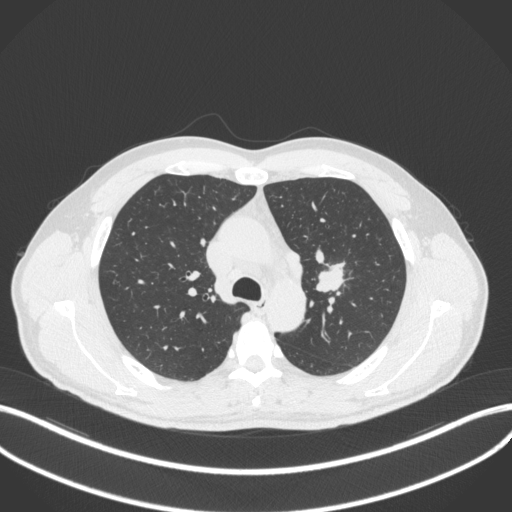
Chest CT, one axial slice. Slice 294 of 383 in the series (ordered by position). Reconstruction kernel B31f. Lung window (W 1500 / L -600 HU). 1 mm slice thickness. 512 × 512 image matrix, field of view 400 × 400 mm. Patient: male, 50 years. From the clinical record (not read from this slice): clinical TNM (as recorded): T1c N1 M1b.
Outlined on this slice (bounding box drawn by a radiologist):
- lung tumour (recorded histology: squamous cell carcinoma): bounding box <315,259,349,294> (left, top, right, bottom; pixels)